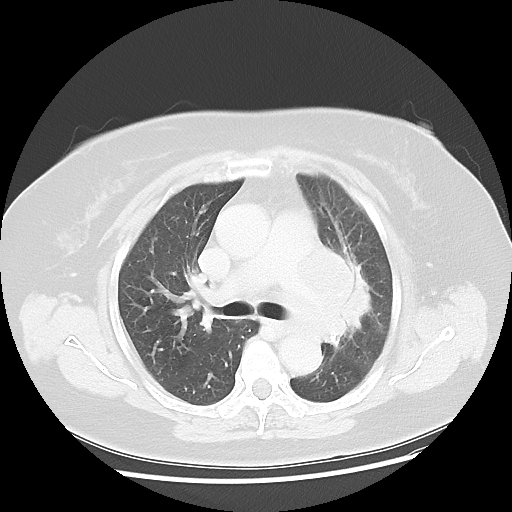
Chest CT, one axial slice; 120 kVp; lung window (W 1500 / L -600 HU); 5 mm slice thickness; 512 × 512 image matrix. Patient: female, 58 years. Case-level facts recorded for this patient, not image findings: clinical TNM (as recorded): T4 N3 M0.
Annotated regions visible in this slice (bounding box drawn by a radiologist):
- lung tumour (recorded histology: small cell carcinoma): bounding box [x1, y1, x2, y2] px = [319, 234, 387, 359]